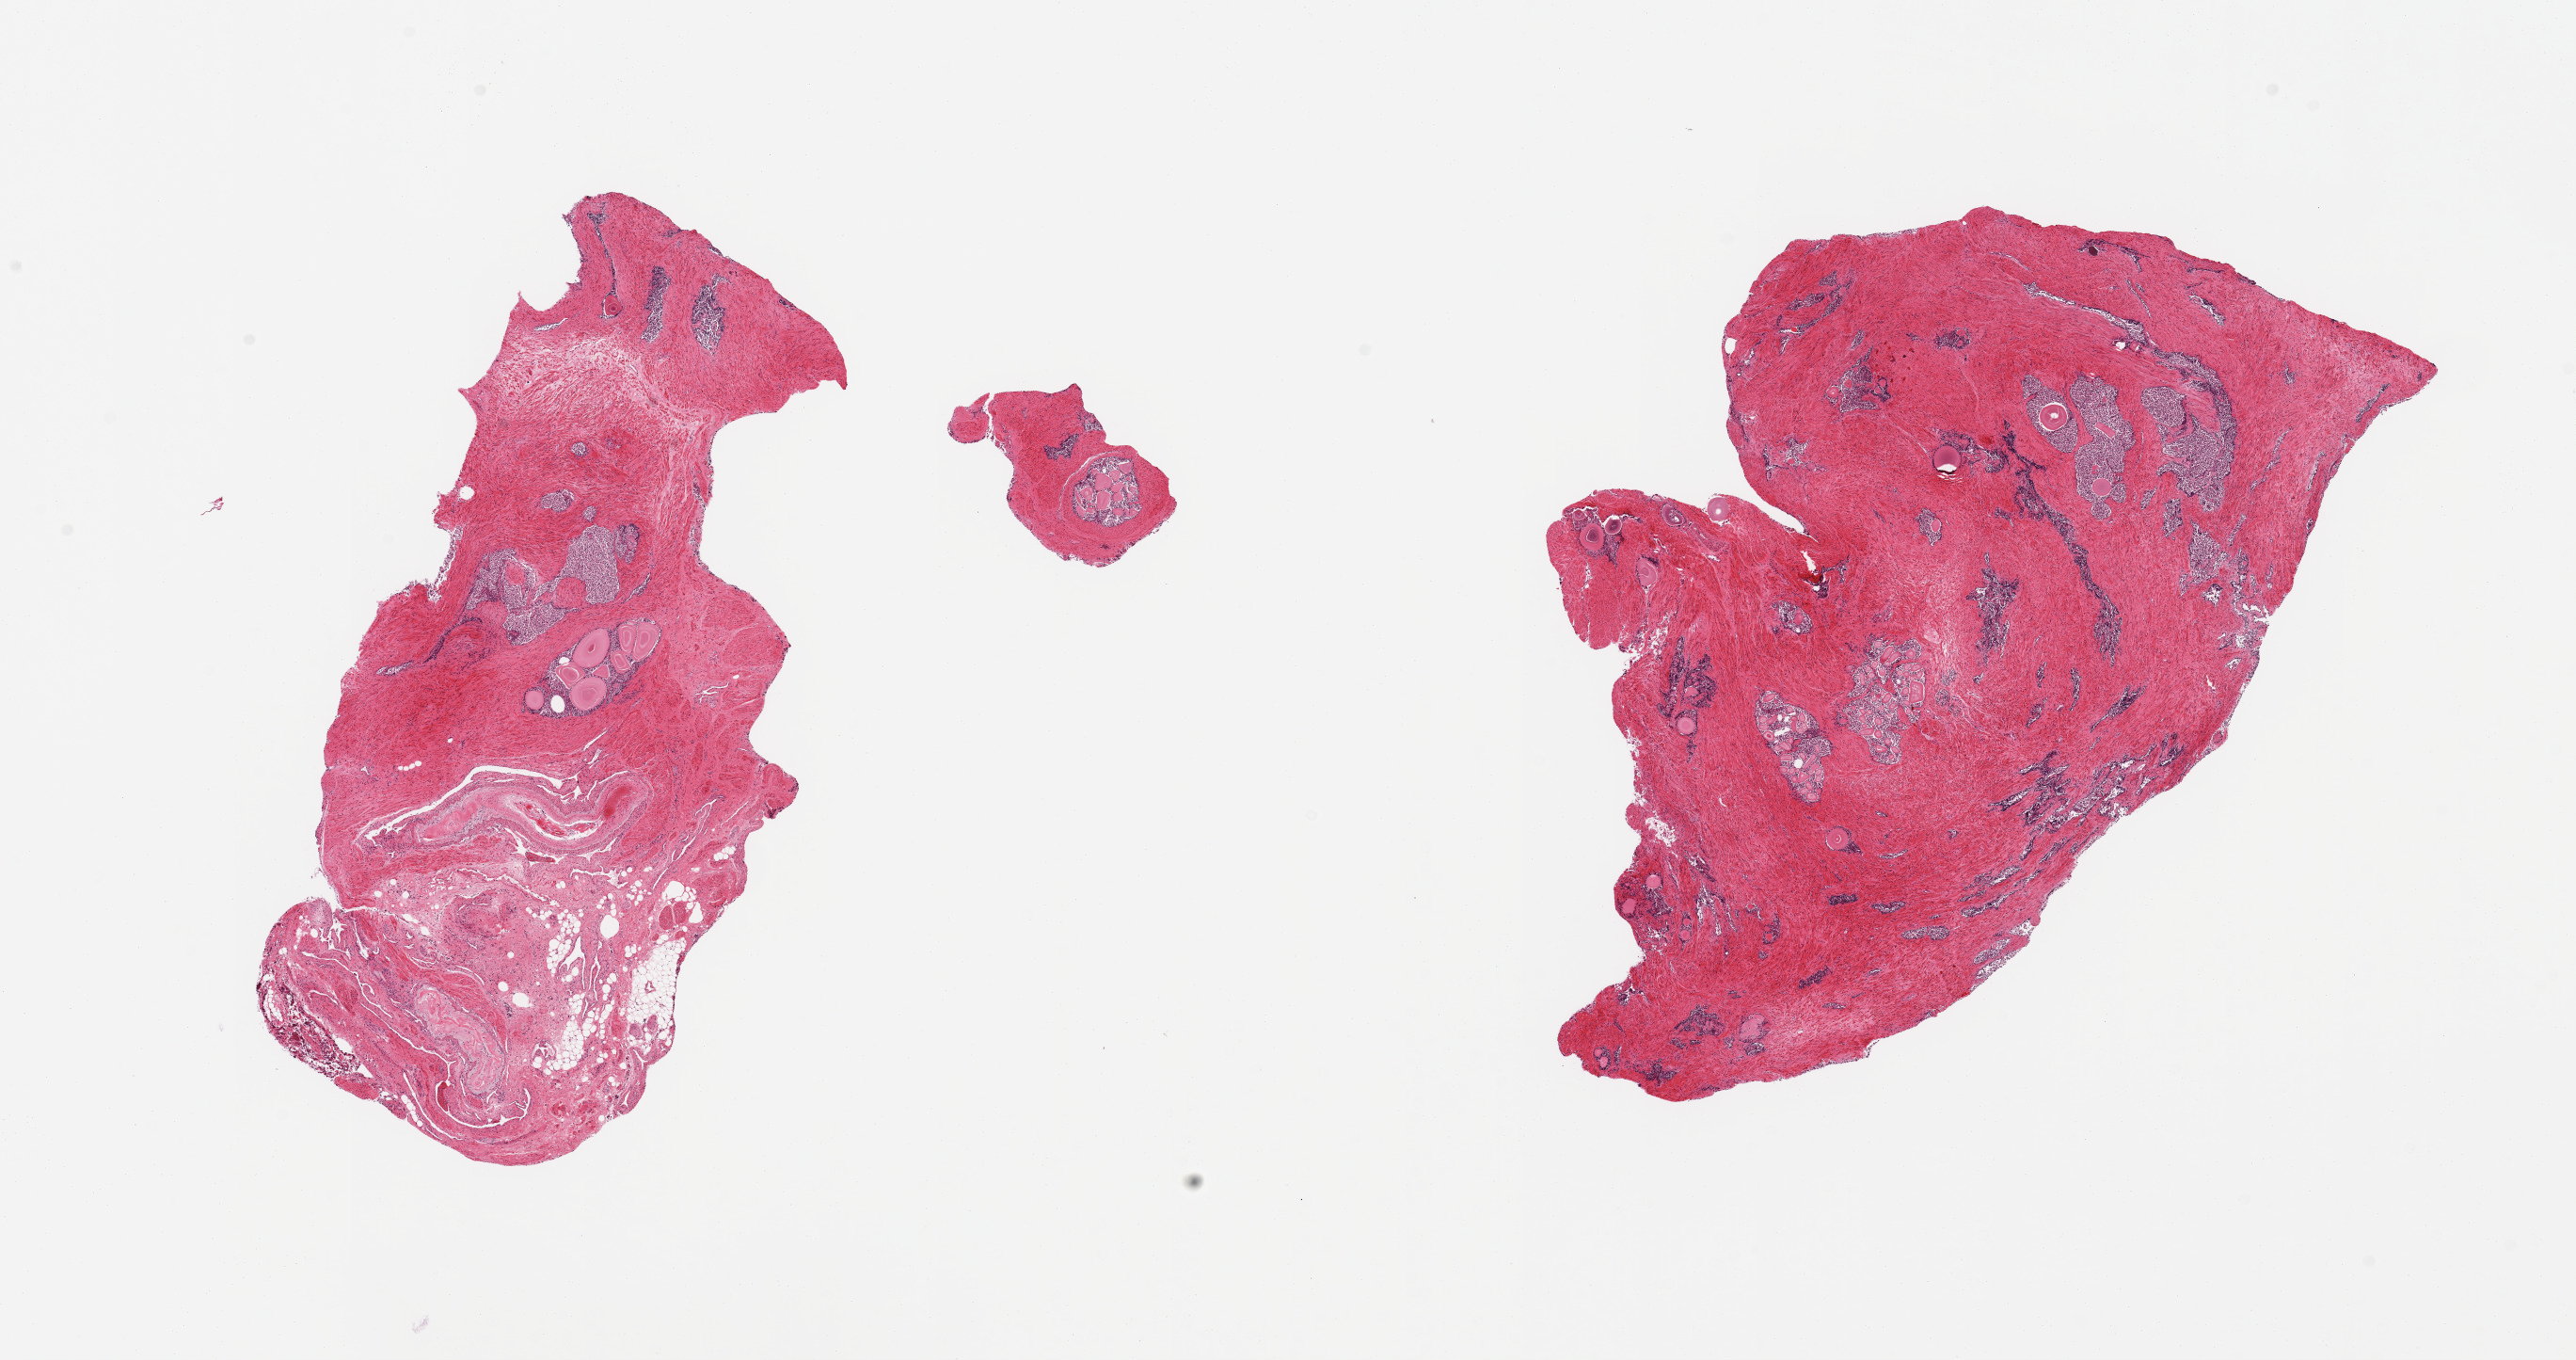
Whole-slide image, hematoxylin and eosin (H&E) stain — a low-resolution overview of the entire scanned area, about 21.7 x 11.4 mm. PAXgene-fixed, paraffin-embedded tissue. Section of prostate (target tissue). Donor tissue sample.
• reviewer comment on this tissue sample: 2 pieces; glands autolyzed, muscle intact; 1 piece has 50% extraneous vascularized stroma